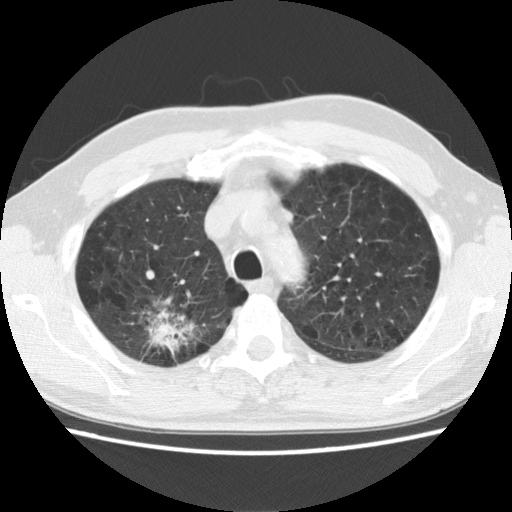
Low-dose screening chest CT, one axial slice. Slice 107 of 142 in the series (ordered by position). 120 kVp. Lung window (W 1500 / L -600 HU). 2.5 mm slice thickness. 512 × 512 image matrix, field of view 340 × 340 mm.
Structures marked on this image (outlined manually by an expert reader):
- lesion 1 (tumor, upper lobe of right lung): bounding box <153,322,176,344> (left, top, right, bottom; pixels)